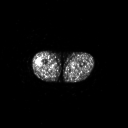
FDG PET of an extremity soft-tissue mass (from a PET/CT study), one axial slice. Slice 224 of 267 in the series (ordered by position). 3.27 mm slice thickness. 128 × 128 image matrix, field of view 700 × 700 mm. Patient: male, 43 years. Case-level facts recorded for this patient, not image findings: histological type: poorly differentiated synovial sarcoma; grade: high; site of the primary tumour: right buttock.
Annotated regions visible in this slice (expert contour drawn on MRI and transferred to this co-registered scan by the dataset authors):
- gross tumour volume including surrounding oedema: bounding box <35,59,43,68> (left, top, right, bottom; pixels)